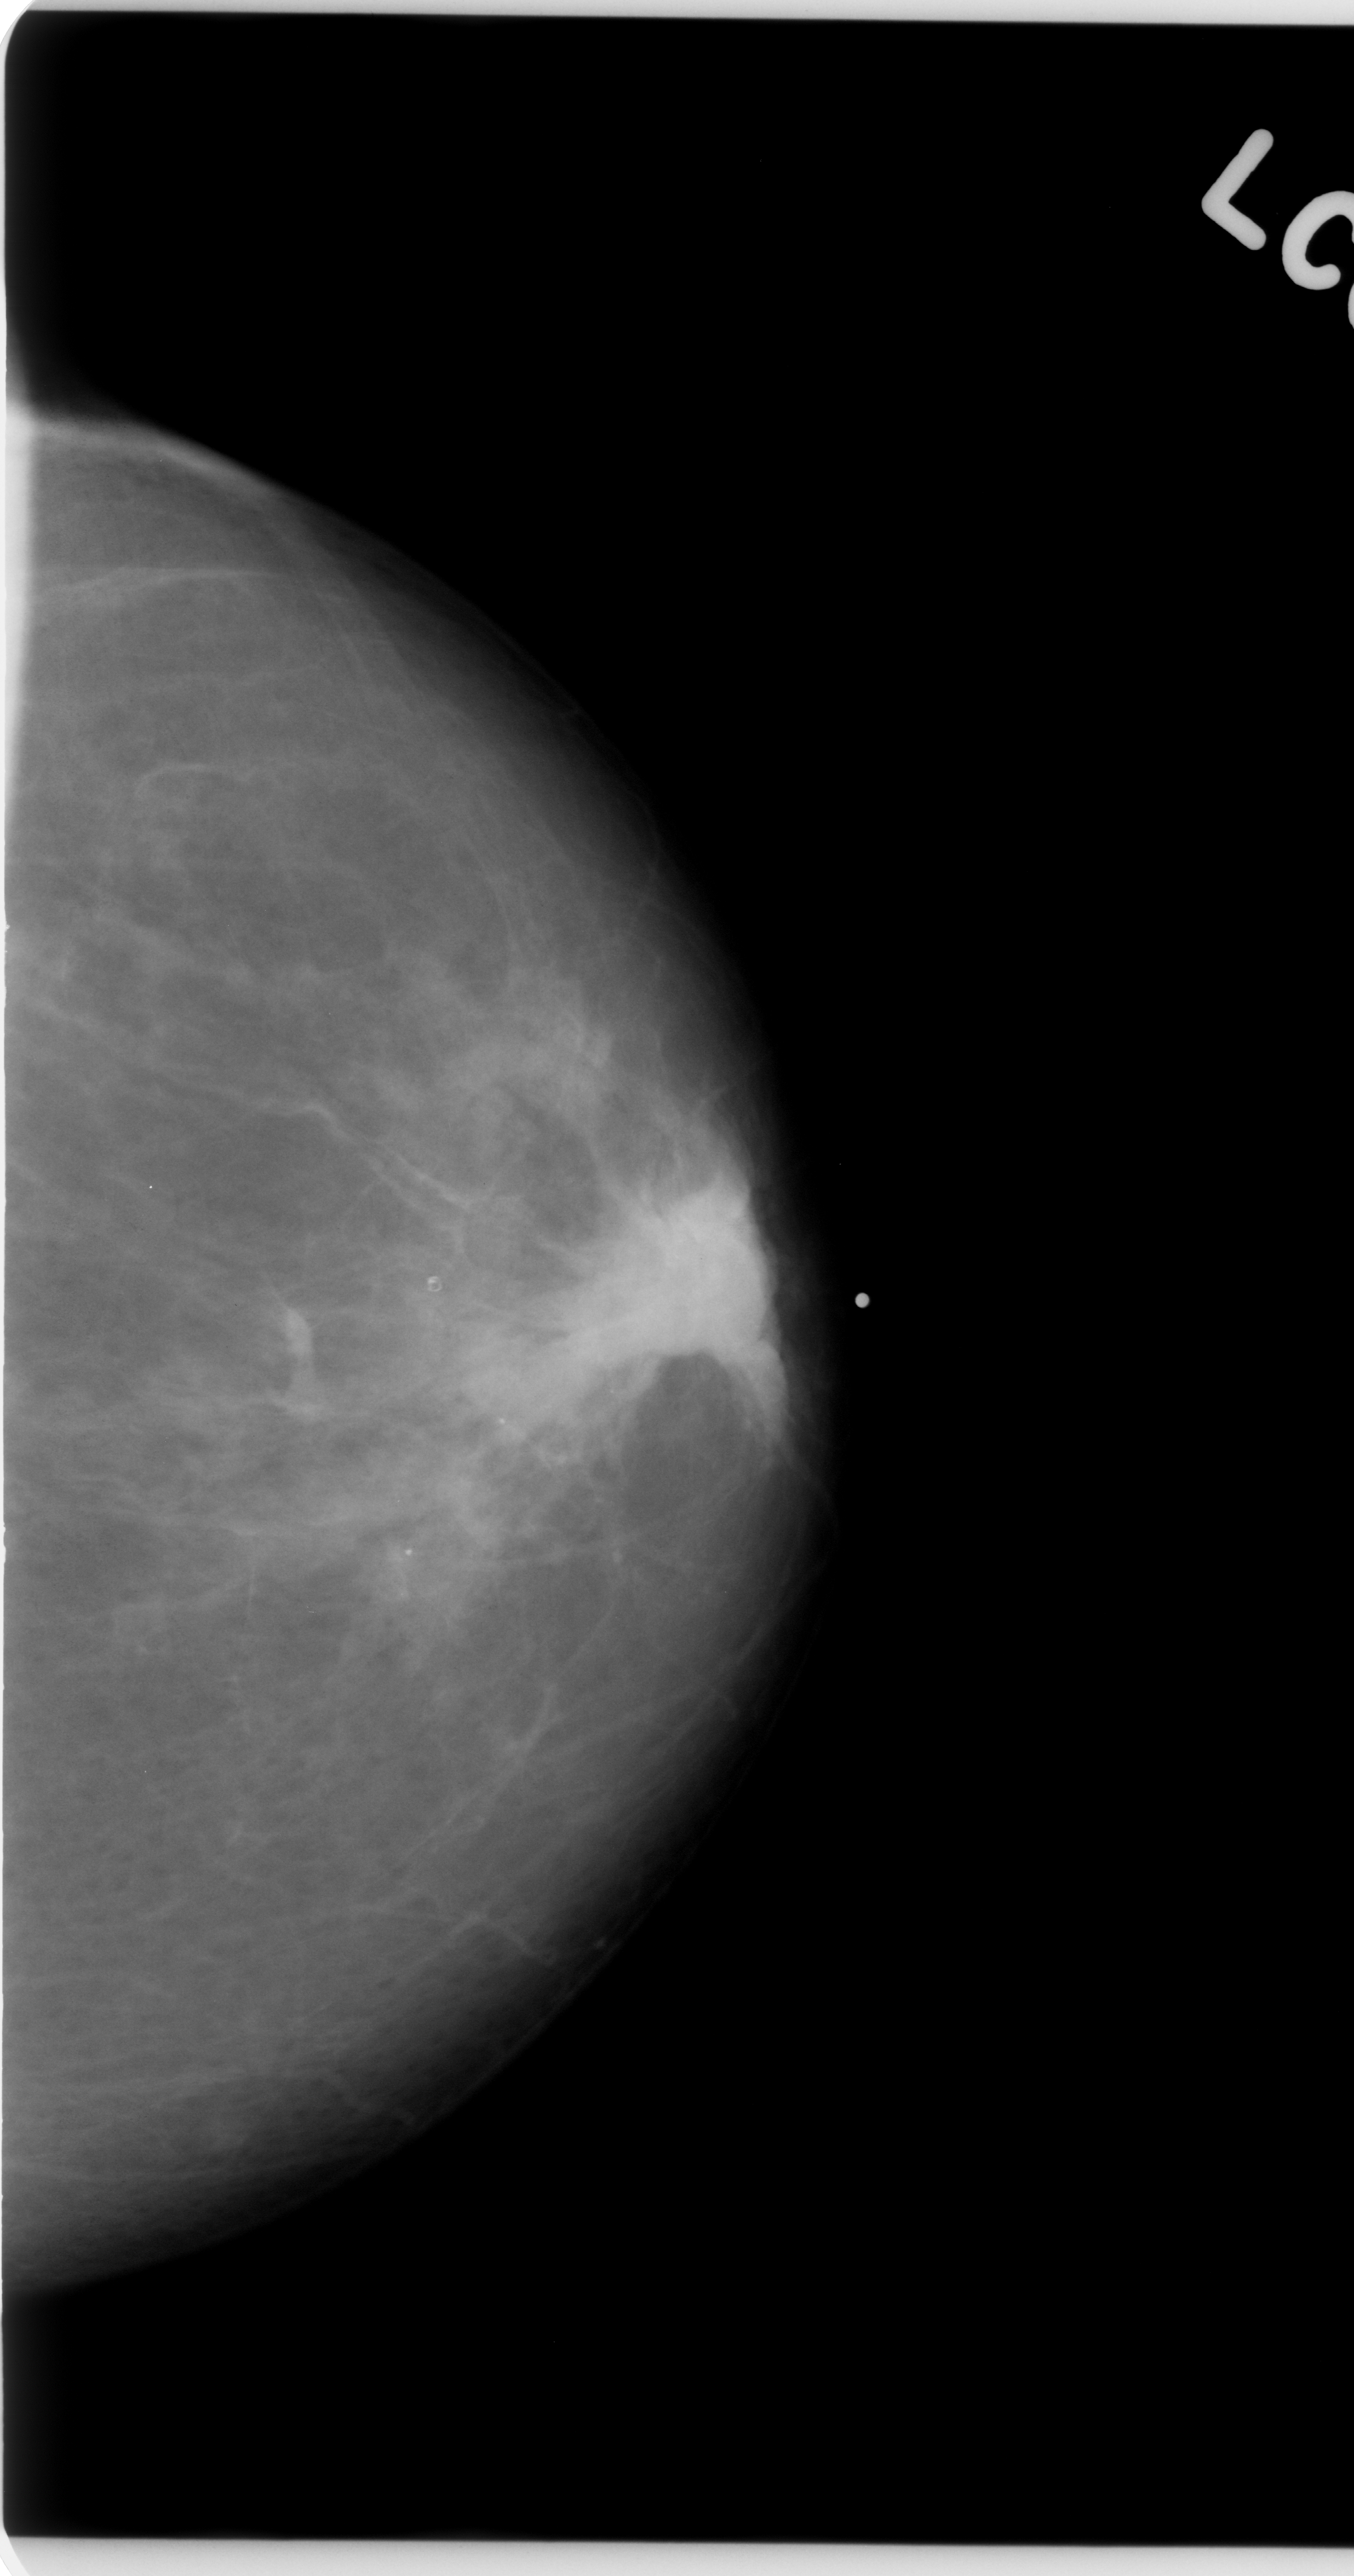
Scanned film-screen mammogram; left breast; CC view; BI-RADS breast density category 2 (scale 1–4); 1354 × 2576 image matrix.
Expert-marked regions of interest on this film, with their recorded descriptors:
- mass, shape irregular, margins spiculated; BI-RADS assessment category 5; subtlety rating 5 on a 1 (subtle) to 5 (obvious) scale; pathology (as recorded): malignant: box from (x=535, y=1079) to (x=840, y=1476) px